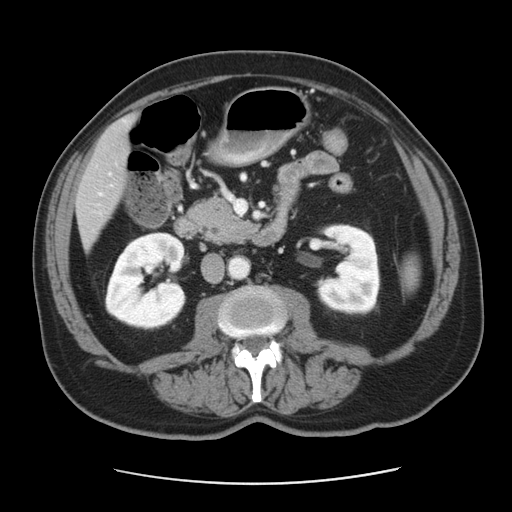
Contrast-enhanced abdominal CT, one axial slice; slice 15 of 42 in the series (ordered by position); reconstruction kernel STANDARD; 120 kVp; intravenous contrast given; soft-tissue window (W 400 / L 40 HU); 512 × 512 image matrix, field of view 370 × 370 mm. Male patient, age 73 years. Case-level facts recorded for this patient, not image findings: diagnosis: colorectal cancer liver metastases, imaged before liver resection; multiple liver metastases: yes; largest metastasis: 0.5 cm; disease in both lobes: no.
Outlined on this slice (outlined manually by an expert reader):
- liver: bounding box [x1, y1, x2, y2] px = [78, 121, 130, 244]
- planned liver remnant (the part of the liver to remain after resection): [108, 120, 130, 147]